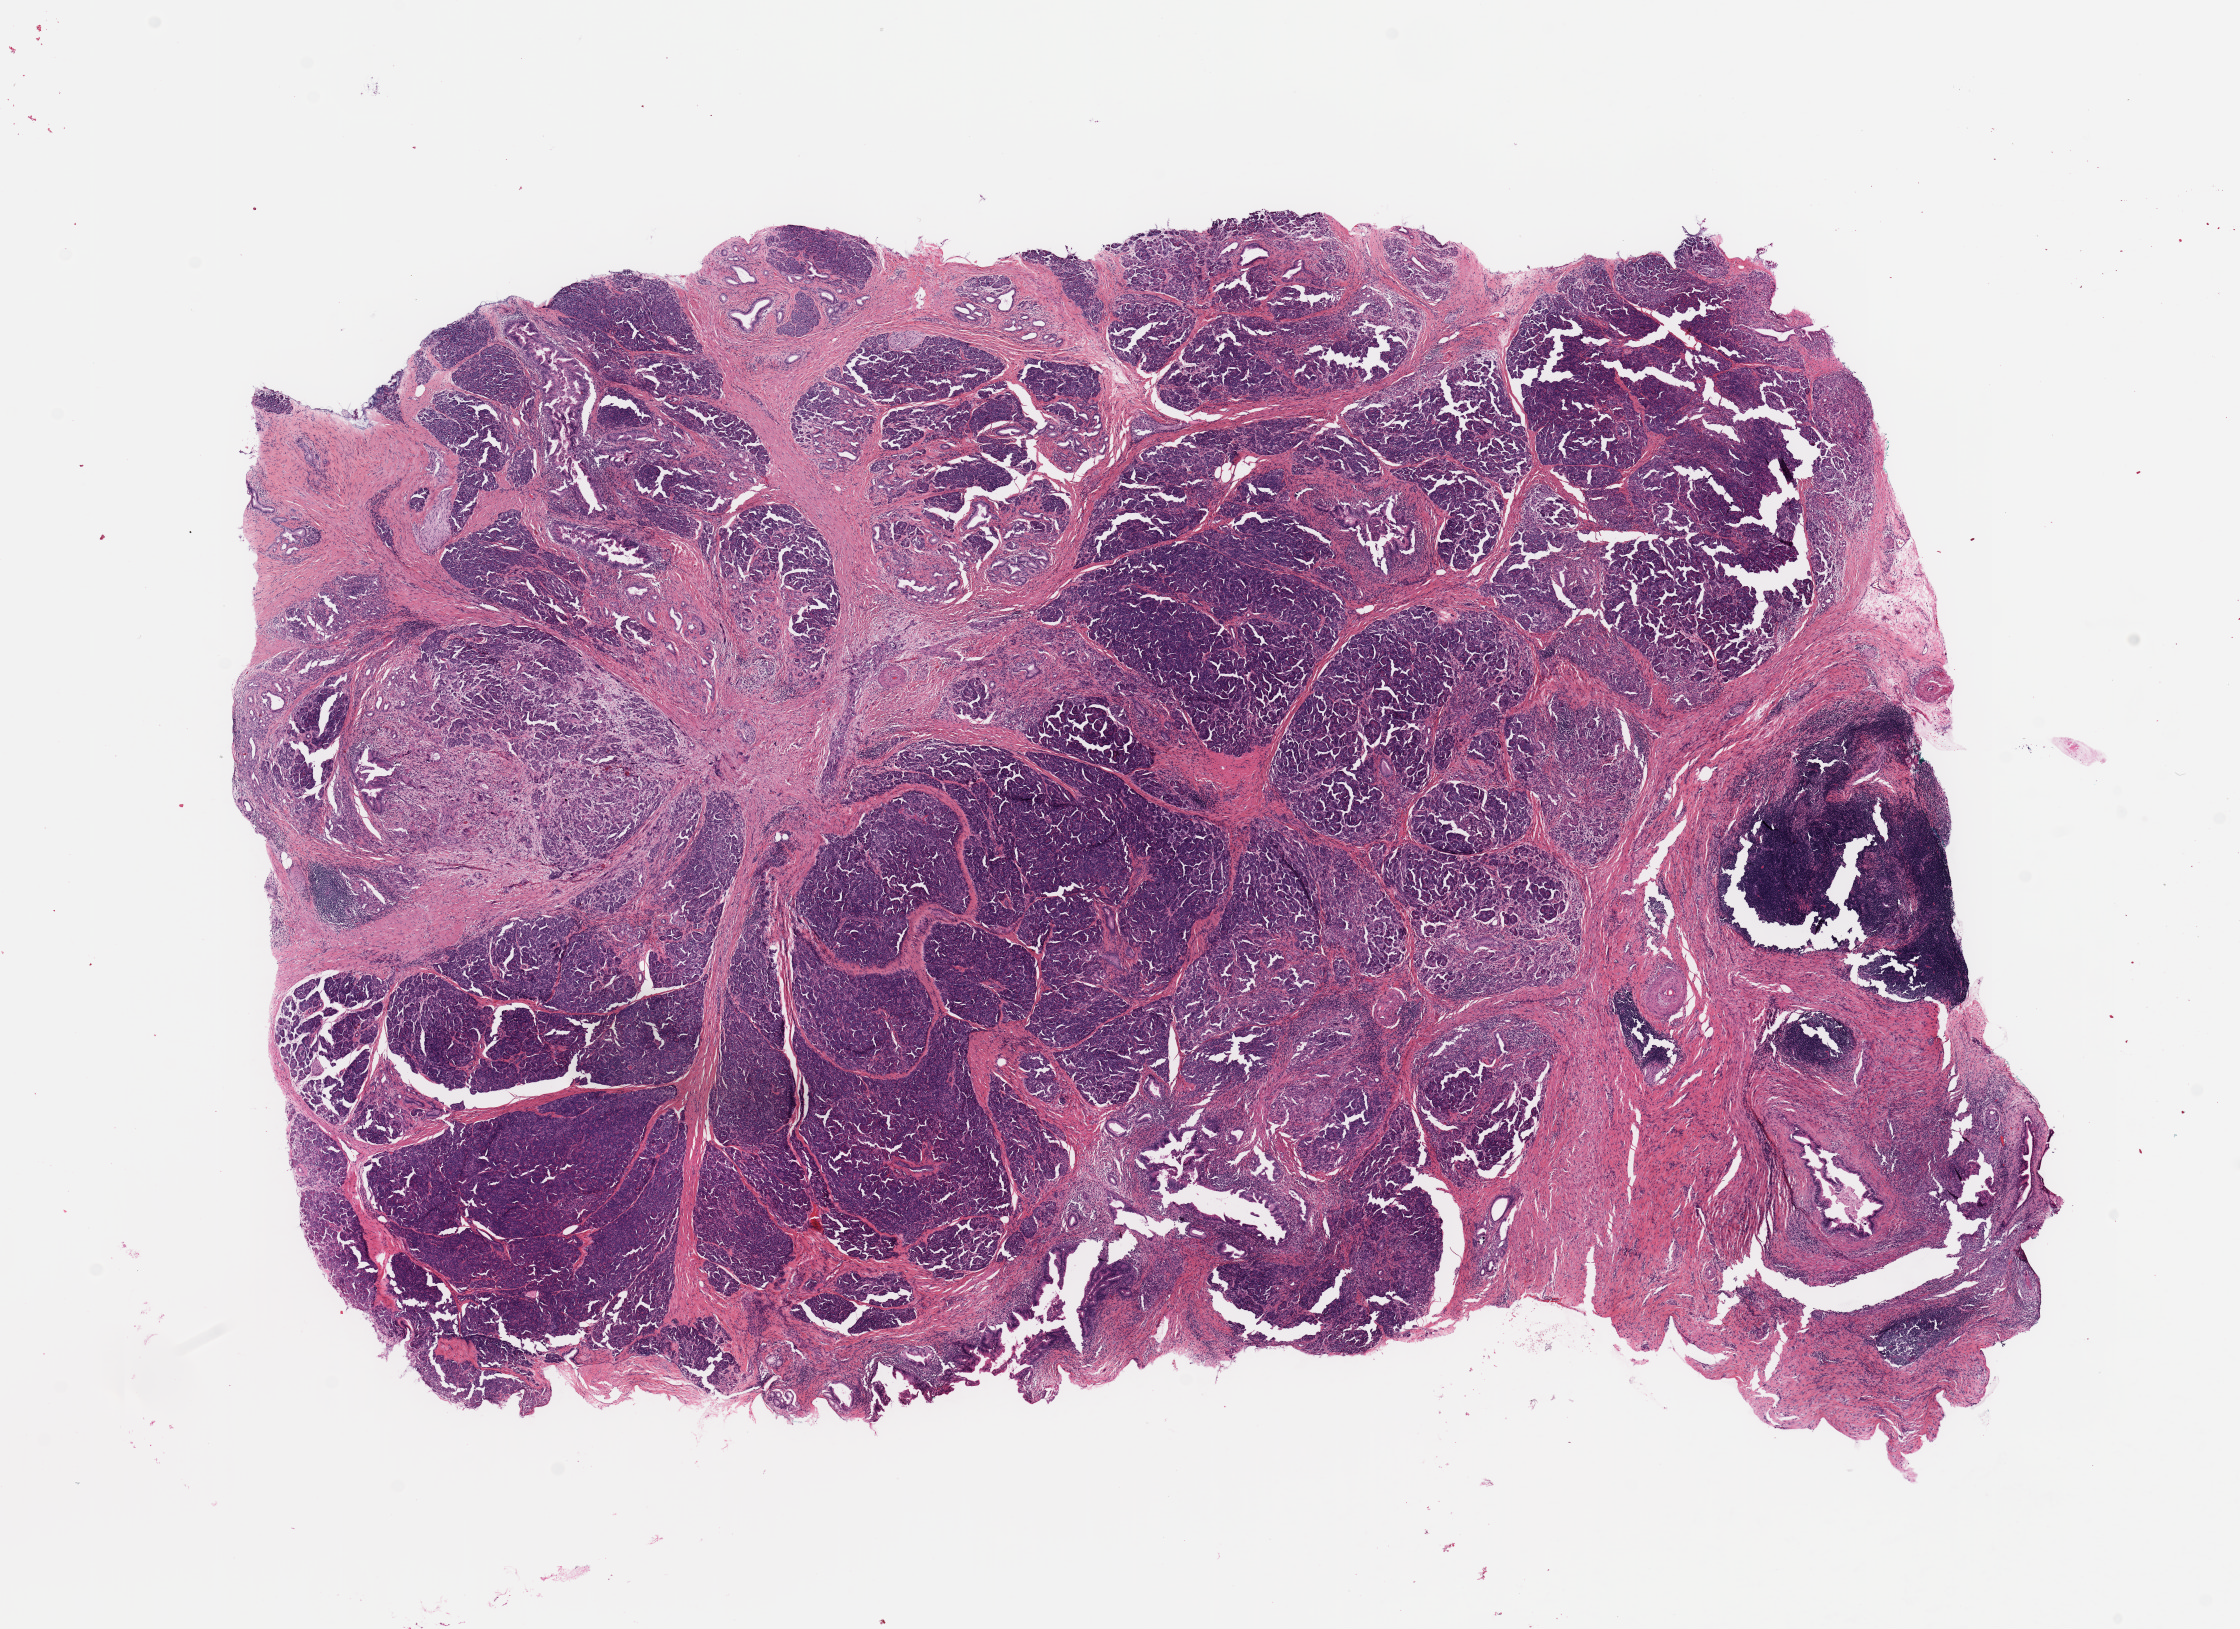
Hematoxylin and eosin (H&E) stained whole-slide image, low-resolution overview of the scanned area, about 17.7 x 12.9 mm. Tumour tissue sample, pancreas. Male, 42 y/o.
Diagnosis: Infiltrating duct carcinoma, NOS.